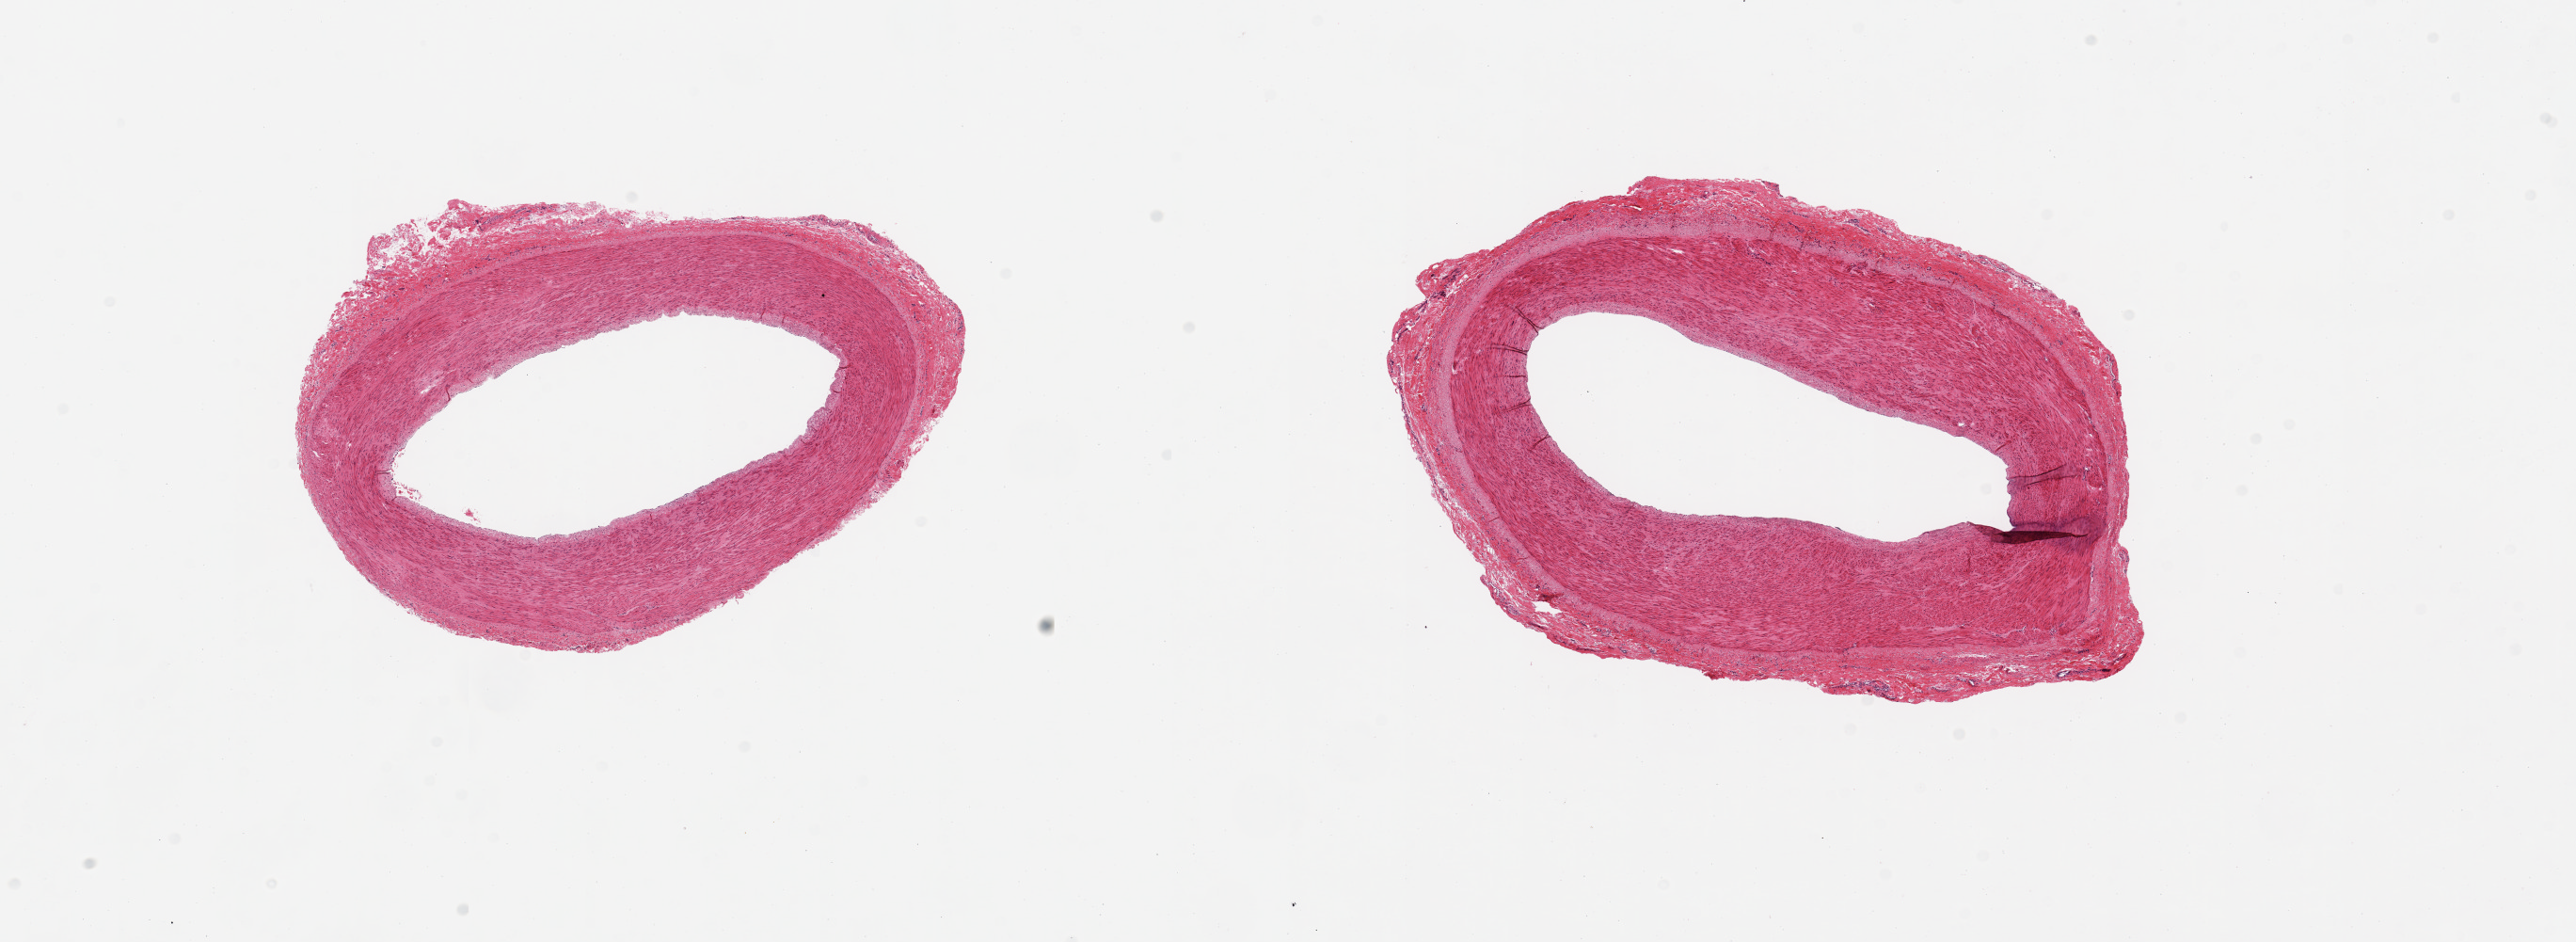
Whole-slide image, haematoxylin and eosin stain — low-resolution overview of the scanned area, about 21.7 x 7.9 mm (from a 20x scan), PAXgene-fixed, paraffin-embedded tissue, section of tibial artery (target tissue), tissue donor sample. Donor sex: male.
Reviewer comment on this tissue sample: 2 pieces, clean, minimal atherosis, good specimen.